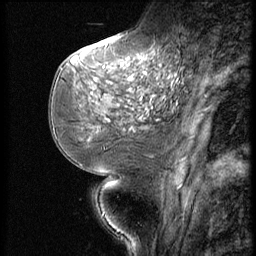
Breast MRI (dynamic contrast-enhanced), one sagittal slice. Slice 23 of 56 in the series (ordered by position). Dynamic contrast-enhanced series, image 2 of 3 at this slice position (ordered by acquisition). 1.5 T. TE 4.2 ms, TR 9 ms. 2.5 mm slice thickness. 256 × 256 image matrix, field of view 180 × 180 mm. Female patient, age 51 years. Case-level facts recorded for this patient, not image findings: setting: breast cancer imaged before/during neoadjuvant chemotherapy; receptor status: triple-negative.
Annotated regions visible in this slice (semi-automatically segmented with operator editing):
- analysis volume of interest (the breast-tissue region the enhancement analysis was run in; not a lesion): bounding box (x1, y1, x2, y2) in pixels: (73, 46, 172, 147)
- tumour enhancement mask (voxels above the 140 % enhancement threshold inside the analysis volume of interest): (130, 54, 154, 79)